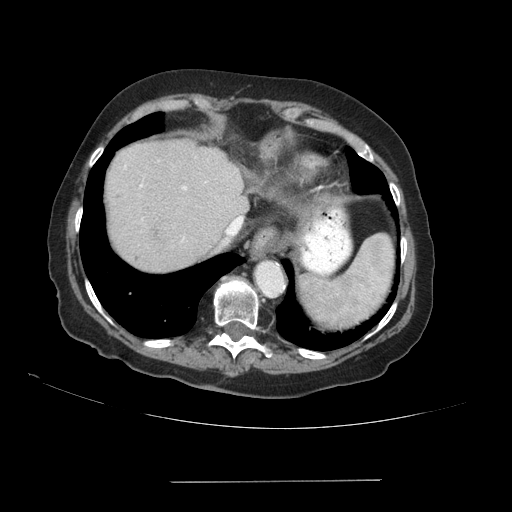
Contrast-enhanced abdominal CT (liver protocol), one axial slice. 140 kVp. Soft-tissue window (W 400 / L 40 HU). 2.5 mm slice thickness. 512 × 512 image matrix, field of view 400 × 400 mm. From the clinical record (not read from this slice): diagnosis: hepatocellular carcinoma (patient treated with transarterial chemoembolisation; whether this scan precedes or follows treatment is not stated here); TNM stage (as recorded): Stage-IVA; Child-Pugh class: A; tumour nodularity: uninodular.
Outlined on this slice (semi-automatic segmentation, software-assisted and operator-edited):
- liver parenchyma outside the tumour (the mass and vessels are separate outlines, so this box may not span the whole liver): box from (x=104, y=140) to (x=248, y=272) px
- liver vessels: (x=140, y=184)–(x=242, y=220)